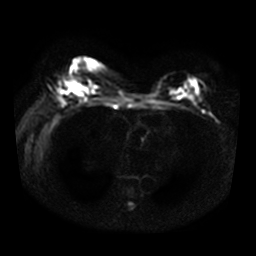
Breast MRI, one axial slice. Position 19 of 34 along the scan axis. Diffusion-weighted series; image 2 of 4 stored at this slice position (different b-values; order by instance number). 3 T. 5 mm slice thickness. 256 × 256 image matrix, field of view 330 × 330 mm. Female patient.
Annotated regions visible in this slice (manually delineated by an expert):
- tumour on diffusion-weighted imaging: box from (x=69, y=82) to (x=86, y=94) px